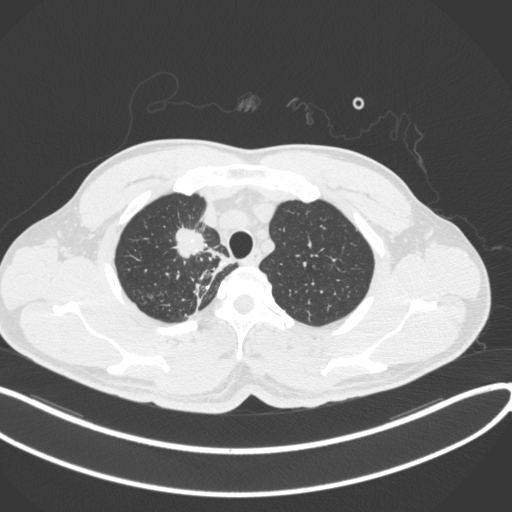
Chest CT, one axial slice. Position 317 of 391 along the scan axis. Reconstruction kernel B31f. 120 kVp. Lung window (W 1500 / L -600 HU). 1 mm slice thickness. 512 × 512 image matrix, field of view 400 × 400 mm. Male patient, age 48 years. From the clinical record (not read from this slice): clinical TNM (as recorded): T1c N1 M1.
Annotated regions visible in this slice (rectangle marked by the reading radiologist):
- lung tumour (recorded histology: adenocarcinoma): bounding box <169,225,210,262> (left, top, right, bottom; pixels)